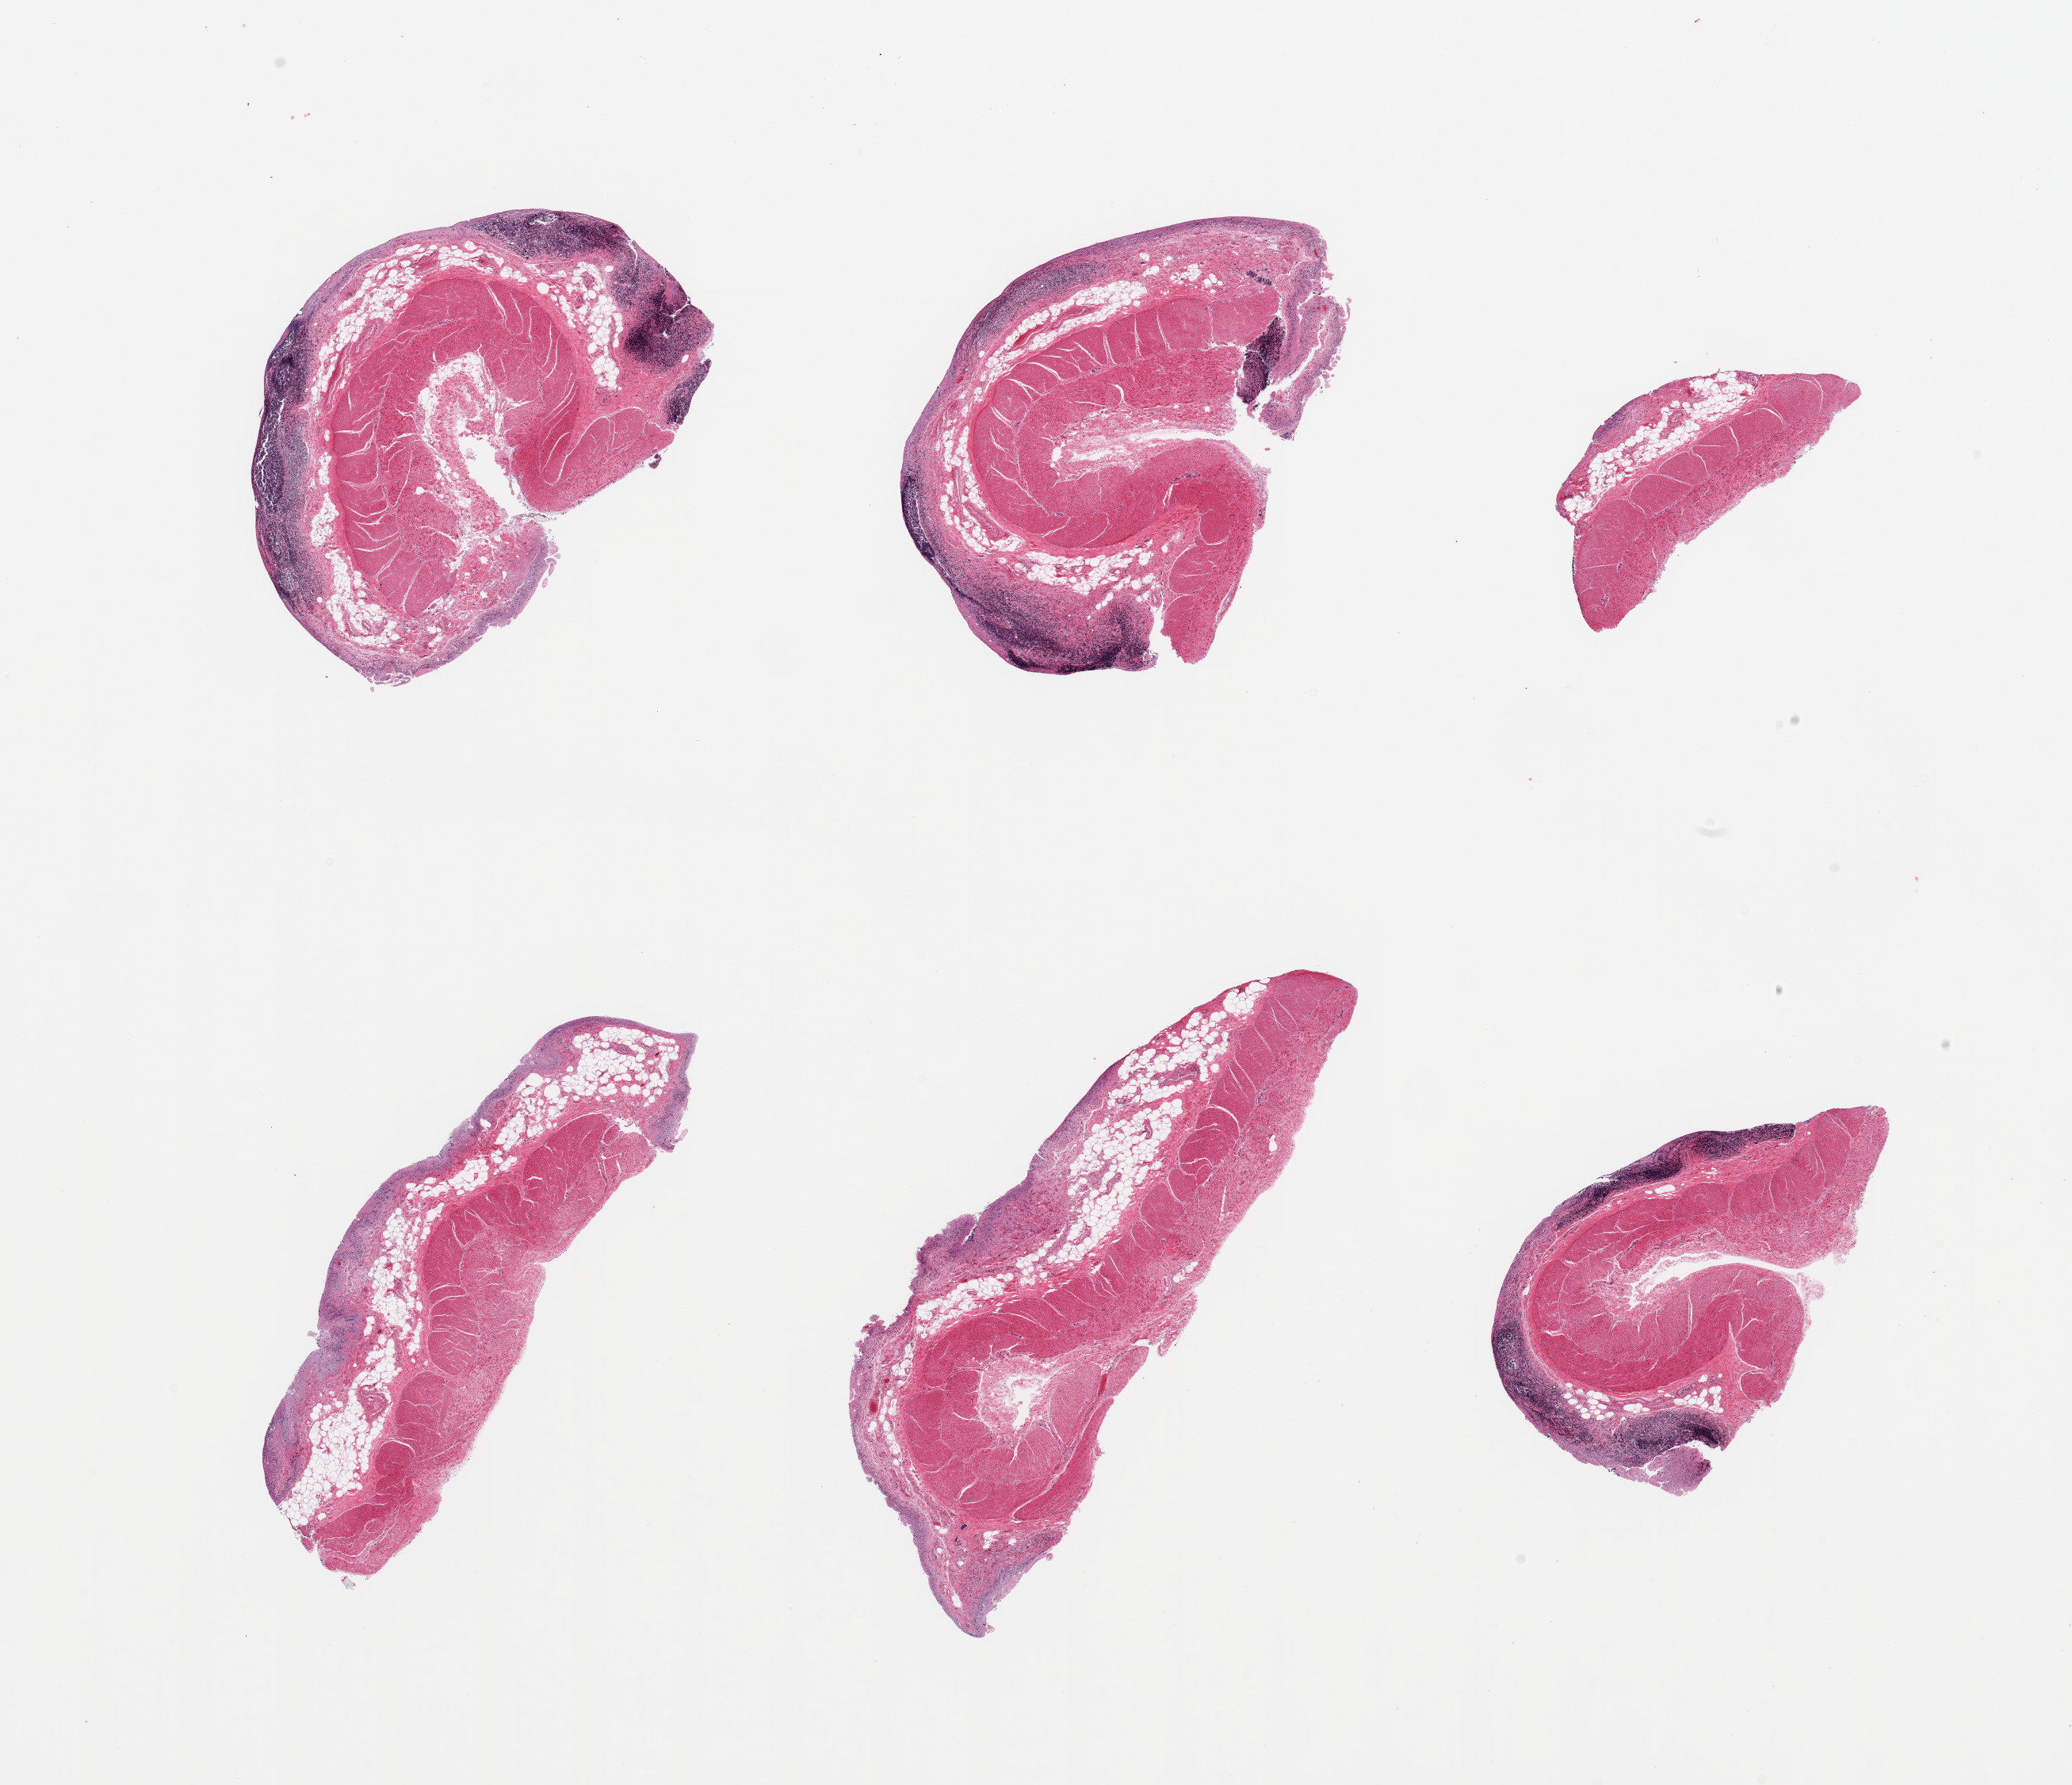
Digitized haematoxylin and eosin-stained section — whole scanned area (about 20.7 x 17.8 mm) shown as a low-resolution overview, PAXgene-fixed paraffin-embedded (PFPE) section, sampled site (target tissue): ileum, donor tissue sample. Female donor.
Review note (as recorded): 6 pieces, advanced mucosal autolysis, residual target lymphoid aggregates are 10-20% of tissue.